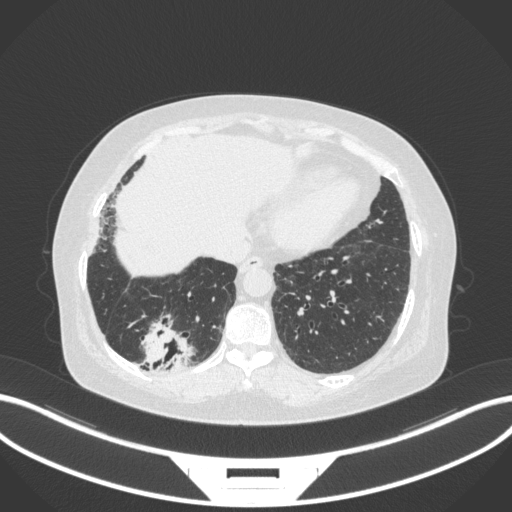
Chest CT, one axial slice; slice 46 of 303 in the series (ordered by position); lung window (W 1500 / L -600 HU); 1 mm slice thickness; 512 × 512 image matrix. Female patient, age 65 years. Case-level facts recorded for this patient, not image findings: clinical TNM (as recorded): T2b N1 M0.
Structures marked on this image (bounding box drawn by a radiologist):
- lung tumour (recorded histology: adenocarcinoma): bounding box <137,312,199,372> (left, top, right, bottom; pixels)